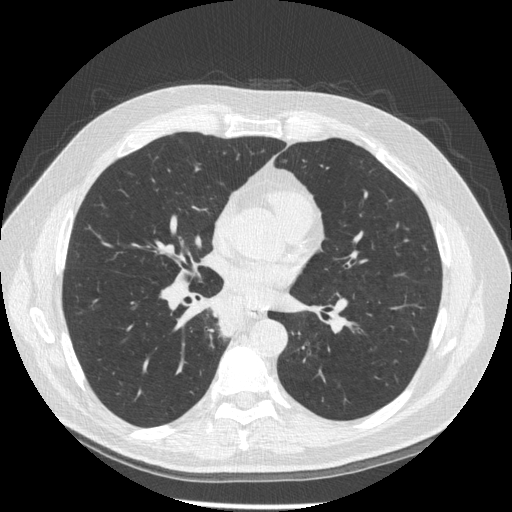
Chest CT (low-dose screening protocol), one axial image; third annual screen; lung window (W 1500 / L -600 HU); 1.25 mm slice thickness; slice 89 of 181 in the series; 512 × 512 image matrix, field of view 370 × 370 mm. Male, age 61 years at enrolment. Former smoker at enrolment.
Expert reader's lesion annotation, box from (x=202, y=298) to (x=256, y=350) px. Screening reader's record for this exam: no non-calcified nodule ≥4 mm recorded. Participant outcome: lung cancer diagnosed 10 days after this screen — squamous cell carcinoma, keratinizing, NOS, right lower lobe, stage IIIB (AJCC 6th edition), 40 mm at pathology.